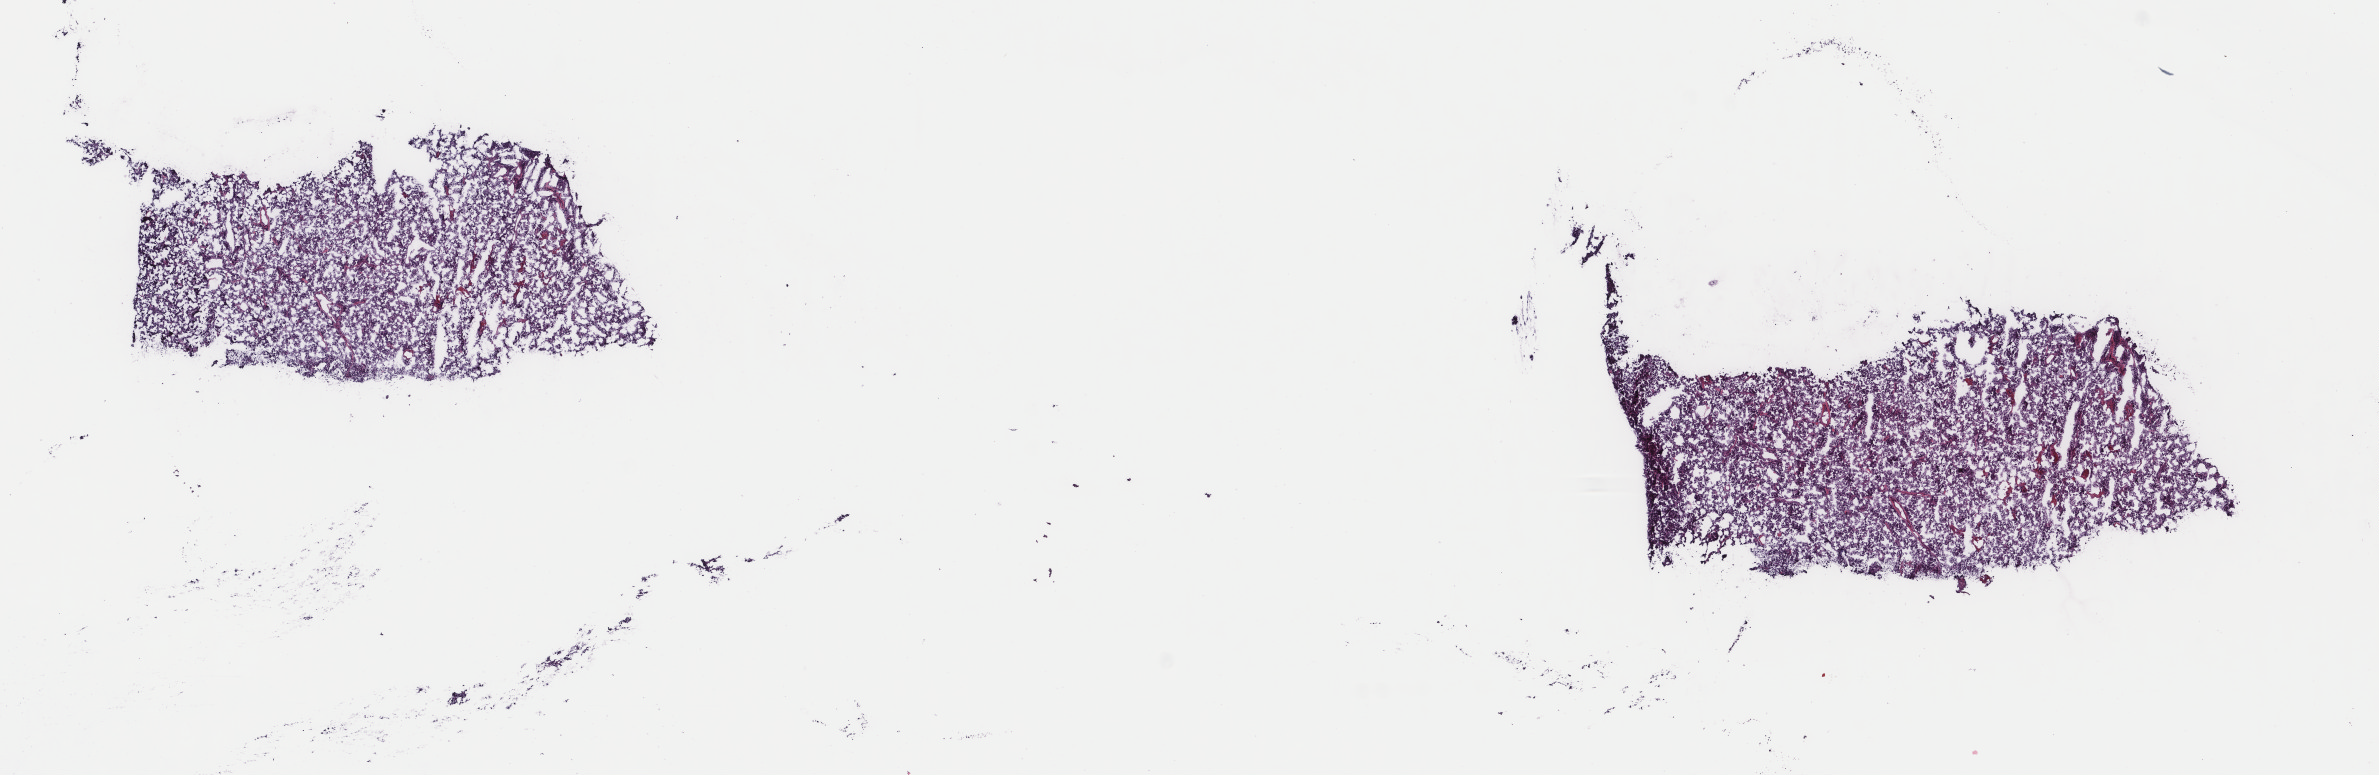
Whole-slide histology image, H&E-stained, low-resolution overview of the scanned area, about 18.9 x 6.2 mm (slide scanned at 40x). Frozen section from the top of the tissue portion. Sample: primary tumour, adrenal gland. Patient: female, age at initial diagnosis 44 years. Pathologist review of this section (percent, as recorded): tumour cells 100%, tumour nuclei 80%, normal cells 0%, stromal cells 0%, necrosis 0%. Inflammatory infiltration, as recorded: lymphocyte infiltration 1%, monocyte infiltration 0%, neutrophil infiltration 0%.
Diagnosis: Pheochromocytoma, NOS.